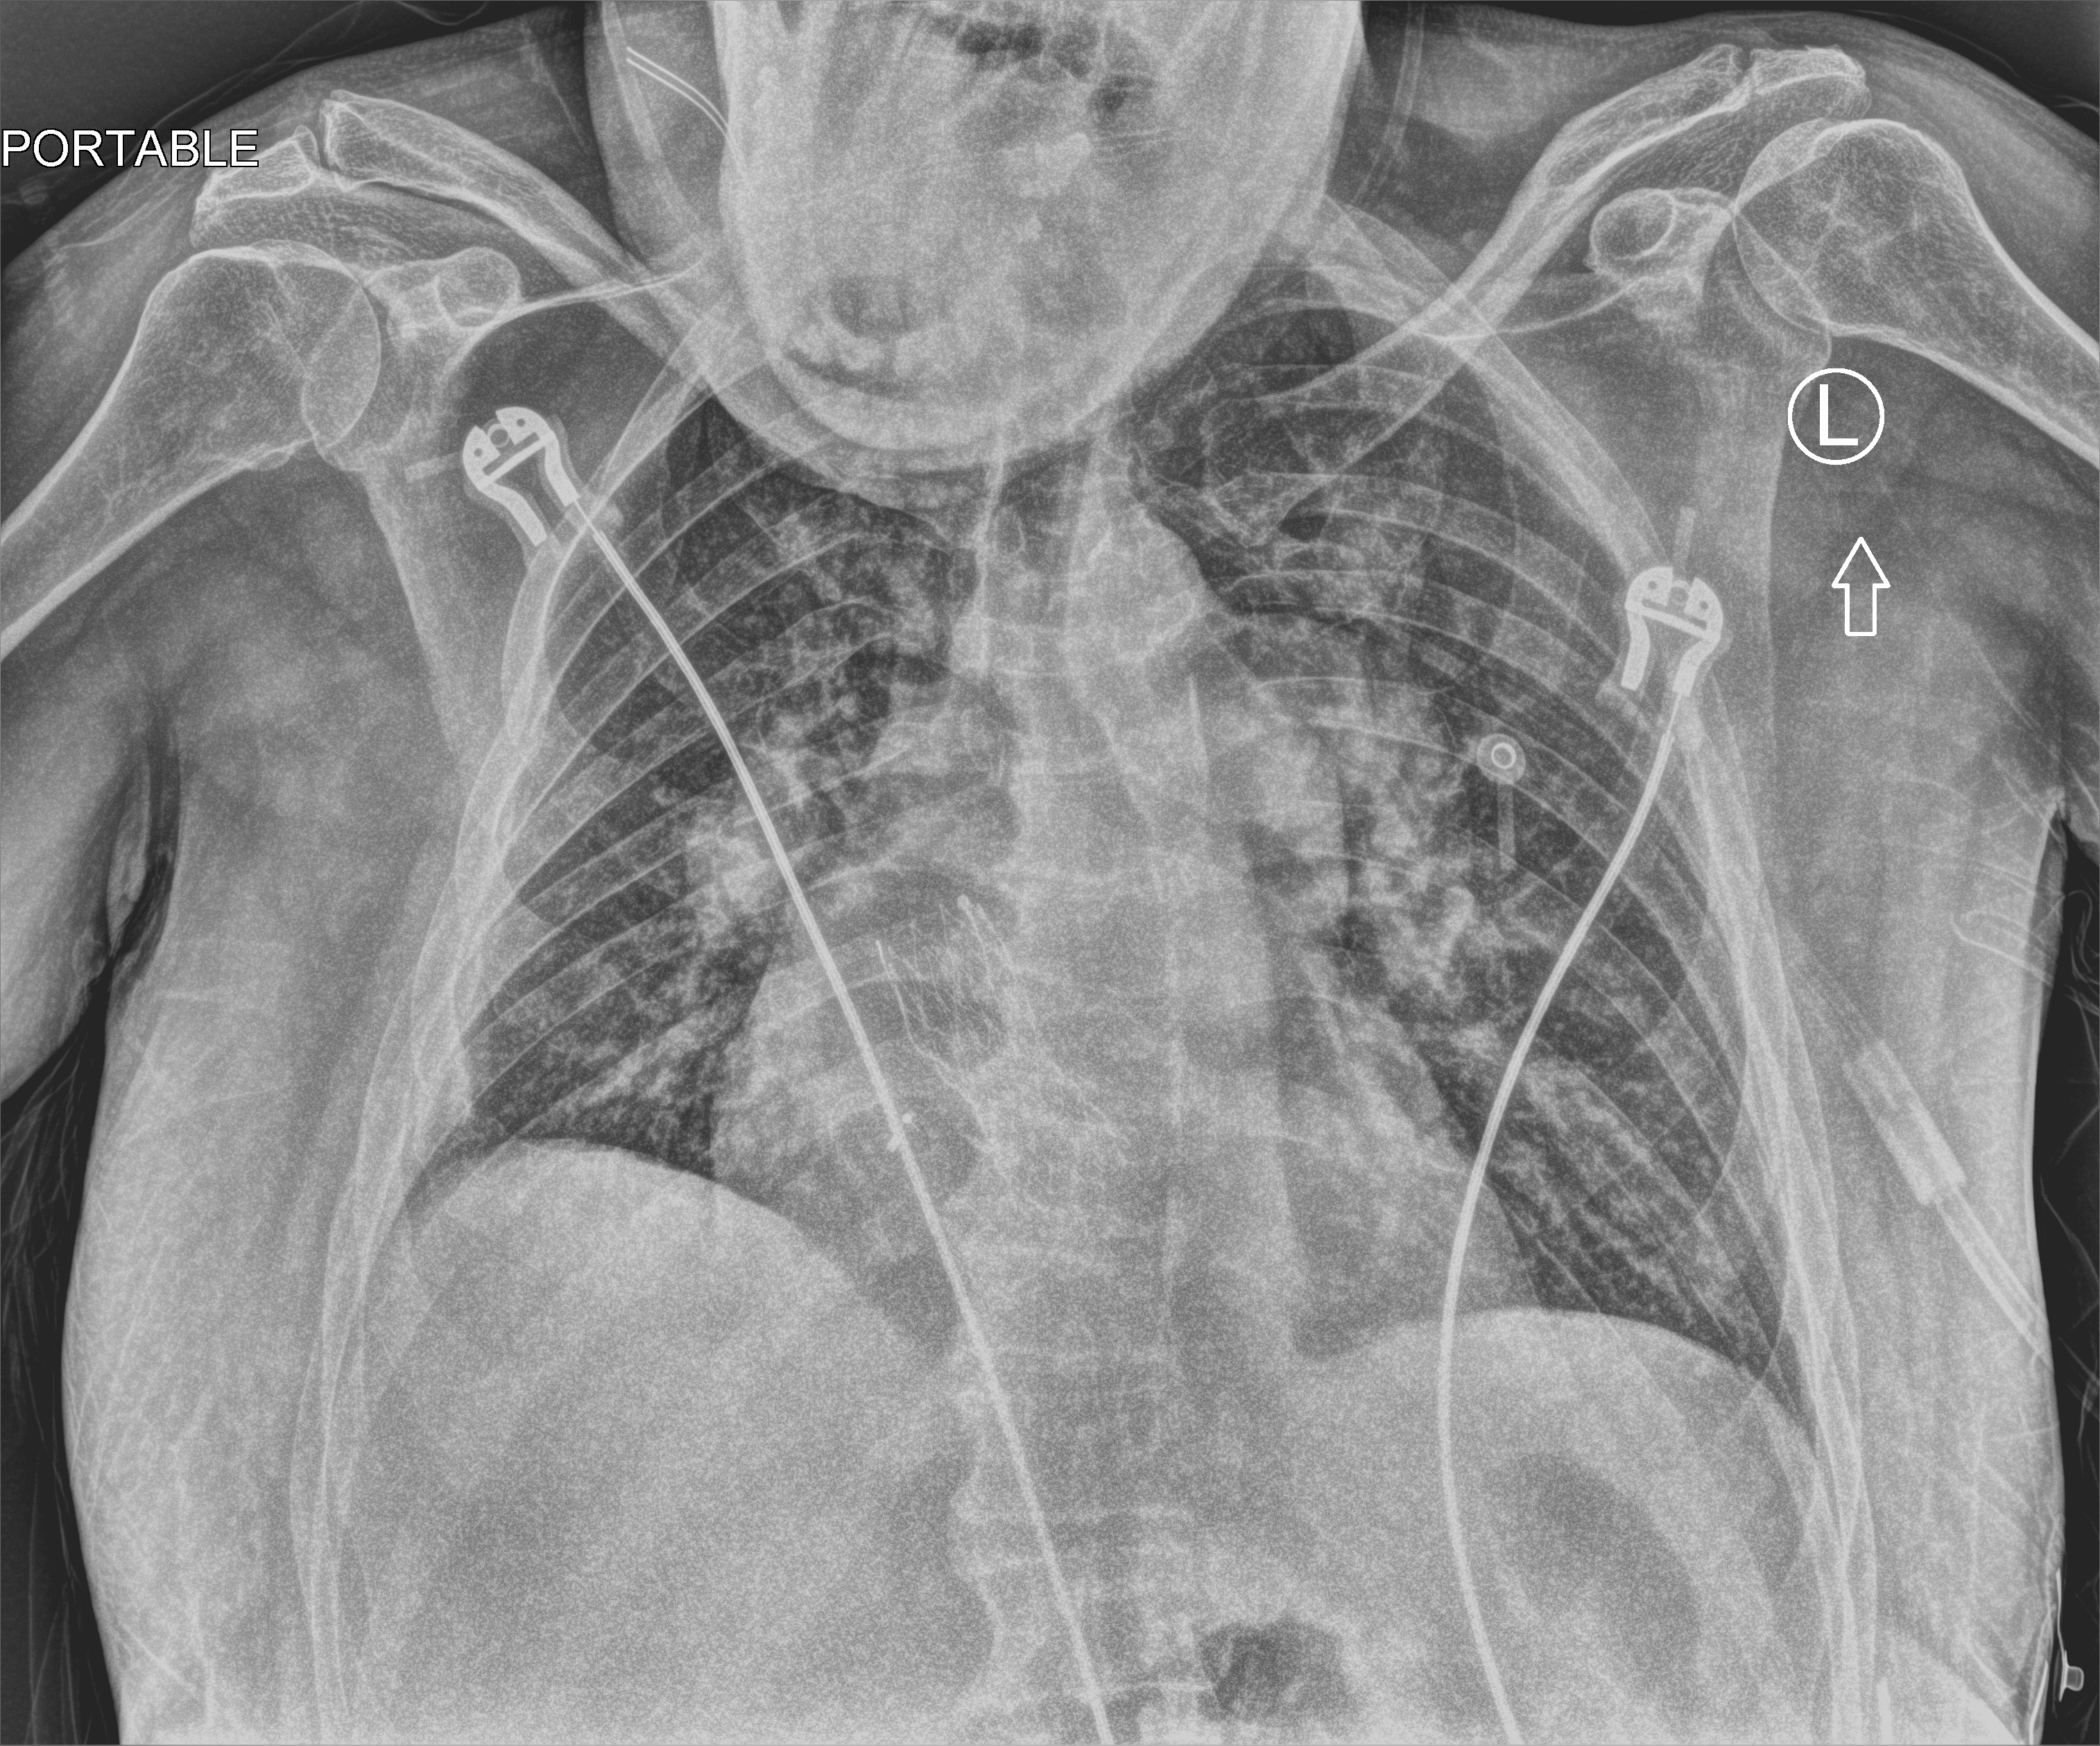
Portable chest radiograph. Patient hospitalised with COVID-19; male, aged 60–74 years.
Hospital-stay facts (about this admission, not read from this image; timing relative to this image not recorded):
- admitted to intensive care during this hospital stay: no